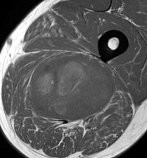
MRI of an extremity soft-tissue mass, one axial slice; position 68 of 86 along the scan axis; MR volume resampled by the dataset authors to the PET/CT grid (not the native acquisition matrix); 147 × 158 image matrix, field of view 144 × 154 mm. Male patient. From the clinical record (not read from this slice): histological type: undifferentiated pleomorphic liposarcoma; grade: high; site of the primary tumour: left thigh.
Structures marked on this image (expert contour drawn on MRI and transferred to this co-registered scan by the dataset authors):
- gross tumour volume including surrounding oedema: bounding box [x1, y1, x2, y2] px = [19, 56, 115, 127]
- gross tumour volume (mass): [30, 56, 115, 118]